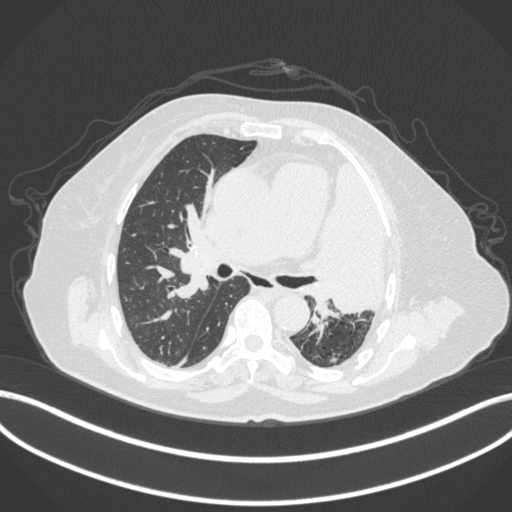
Chest CT, one axial slice. Slice 229 of 399 in the series (ordered by position). Reconstruction kernel B31f. Lung window (W 1500 / L -600 HU). 1 mm slice thickness. 512 × 512 image matrix, field of view 400 × 400 mm. Female patient, age 75 years. Case-level facts recorded for this patient, not image findings: clinical TNM (as recorded): T3 N3 M1.
Structures marked on this image (bounding box drawn by a radiologist):
- lung tumour (recorded histology: adenocarcinoma): bounding box [x1, y1, x2, y2] px = [316, 159, 395, 318]